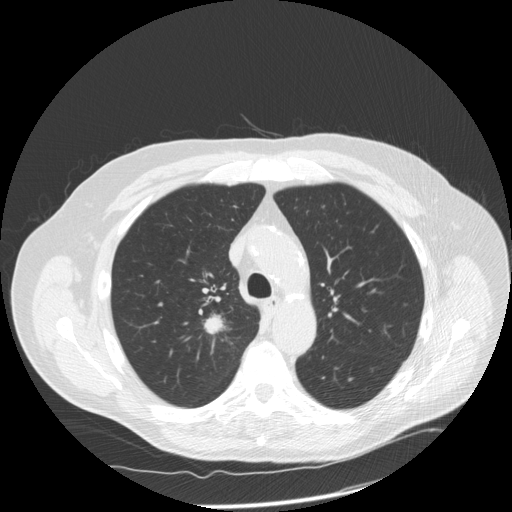
Low-dose screening chest CT, axial slice, third screening round (two years after baseline), lung window (W 1500 / L -600 HU), 2.5 mm slice thickness, 120 kVp. Male, age 69 years at enrolment. Former smoker at enrolment.
• Expert-annotated lung lesion, bounding box [x1, y1, x2, y2] px = [183, 304, 243, 353].
• Reader record for this screening exam (exam-level; its link to the box is not recorded): non-calcified nodule or mass ≥4 mm, right upper lobe, 18 × 17 mm, spiculated (stellate) margins, soft tissue attenuation, pre-existing on the prior screen: no.
• Official screen result: positive, other.
• Lung cancer was diagnosed 13 days after this screen: squamous cell carcinoma, NOS, right upper lobe, poorly differentiated (G3), stage IA (AJCC 6th edition), 22 mm at pathology.